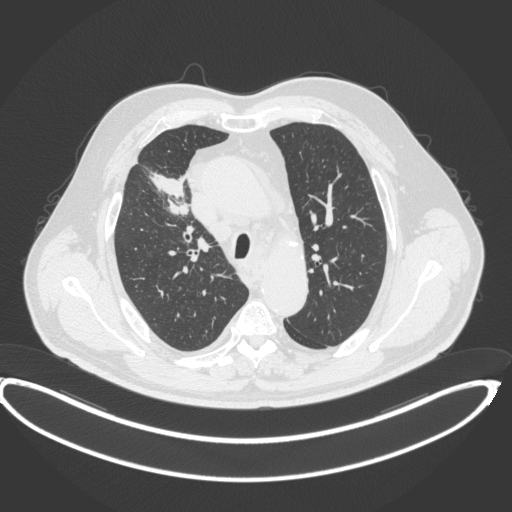
Chest CT, one axial slice. Slice 293 of 395 in the series (ordered by position). Reconstruction kernel B31f. Lung window (W 1500 / L -600 HU). 1 mm slice thickness. 512 × 512 image matrix. Male patient, age 62 years. Case-level facts recorded for this patient, not image findings: clinical TNM (as recorded): T1c N3 M1c.
Outlined on this slice (bounding box drawn by a radiologist):
- lung tumour (recorded histology: adenocarcinoma): box from (x=147, y=169) to (x=193, y=219) px